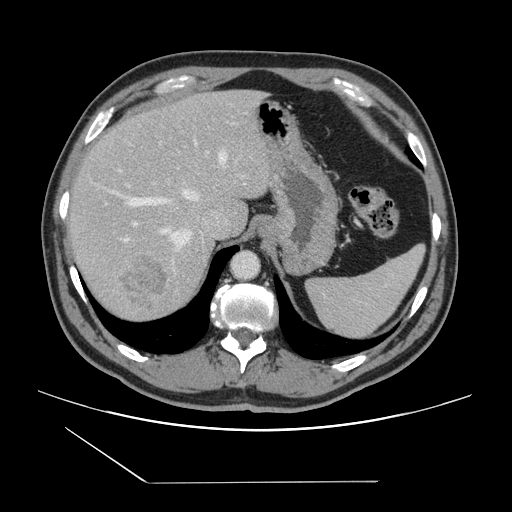
Contrast-enhanced abdominal CT, one axial slice. Slice 113 of 157 in the series (ordered by position). 120 kVp. Intravenous contrast given. Soft-tissue window (W 400 / L 40 HU). 2.5 mm slice thickness. 512 × 512 image matrix, field of view 407 × 407 mm. Male patient, age 61 years. From the clinical record (not read from this slice): diagnosis: colorectal cancer liver metastases, imaged before liver resection; multiple liver metastases: yes; largest metastasis: 5.5 cm.
Annotated regions visible in this slice (manually delineated by an expert):
- hepatic veins: bounding box [x1, y1, x2, y2] px = [118, 151, 227, 274]
- liver: [69, 91, 272, 322]
- planned liver remnant (the part of the liver to remain after resection): [69, 91, 236, 231]
- portal vein (with intrahepatic branches): [127, 143, 244, 226]
- liver metastasis: [117, 253, 169, 311]